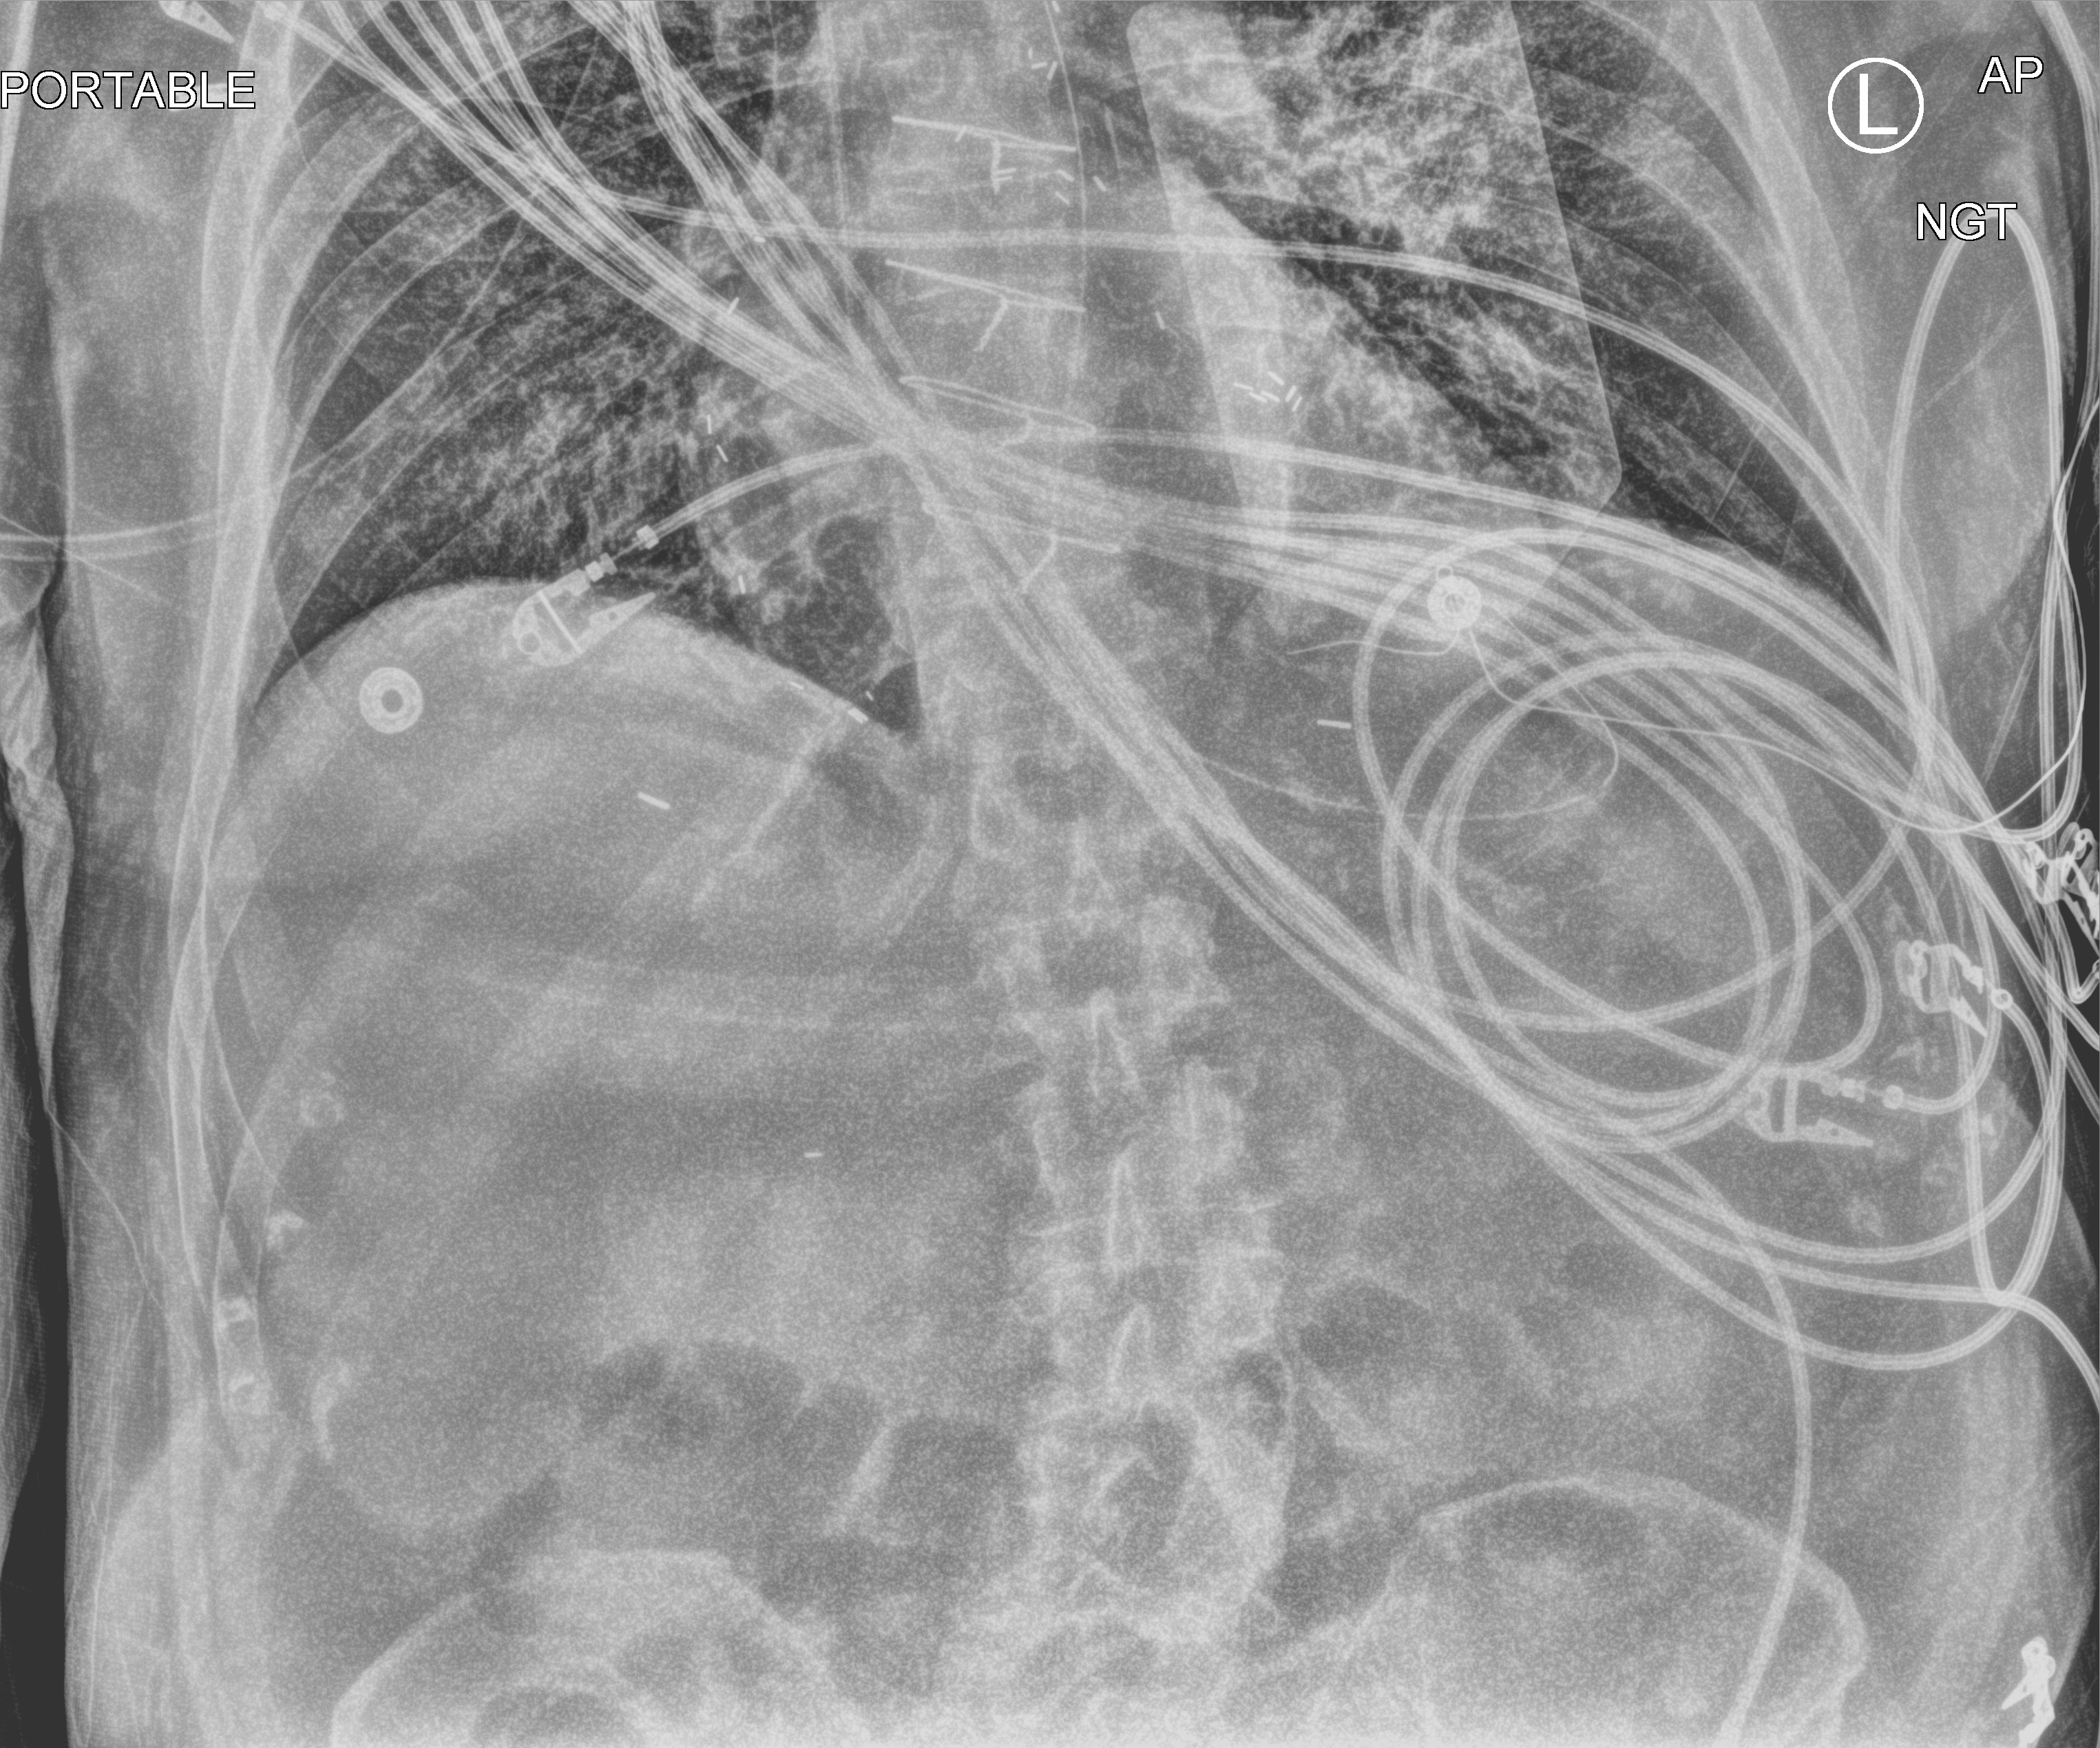
Bedside chest radiograph (computed radiography). Male patient hospitalised with COVID-19, age 75–90 years.
Hospital-stay facts (about this admission, not read from this image; timing relative to this image not recorded):
- other chronic lung disease (admission record): no